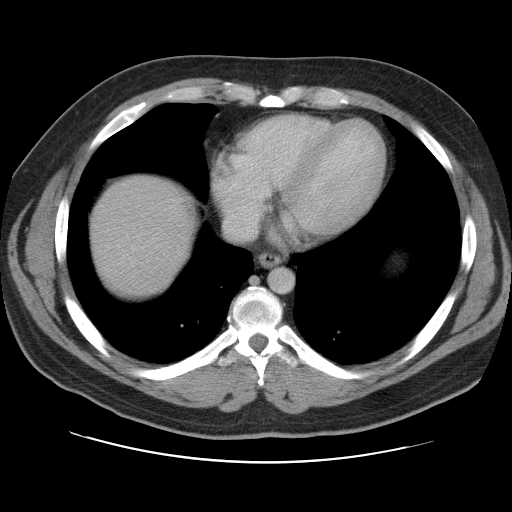
Contrast-enhanced abdominal CT, one axial slice; slice 102 of 109 in the series (ordered by position); soft-tissue window (W 400 / L 40 HU); 512 × 512 image matrix, field of view 402 × 402 mm. Male patient, age 35 years. From the clinical record (not read from this slice): diagnosis: colorectal cancer liver metastases, imaged before liver resection; multiple liver metastases: yes; largest metastasis: 2.8 cm; disease in both lobes: yes.
Outlined on this slice (manually delineated by an expert):
- liver: bounding box (x1, y1, x2, y2) in pixels: (91, 176, 195, 298)
- planned liver remnant (the part of the liver to remain after resection): (90, 176, 195, 298)